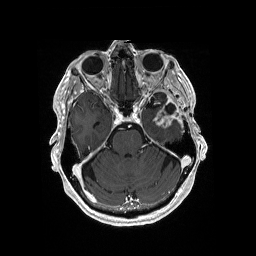
Brain MRI from a brain-tumour surgery series, one axial slice; T1-weighted post-contrast; 256 × 256 image matrix, field of view 256 × 256 mm. Case-level facts recorded for this patient, not image findings: histopathology: Glioblastoma; WHO grade: 4; IDH mutation: no.
Outlined on this slice (manually delineated by an expert):
- previous resection cavity: bounding box (x1, y1, x2, y2) in pixels: (165, 104, 175, 114)
- tumour: (153, 113, 178, 128)